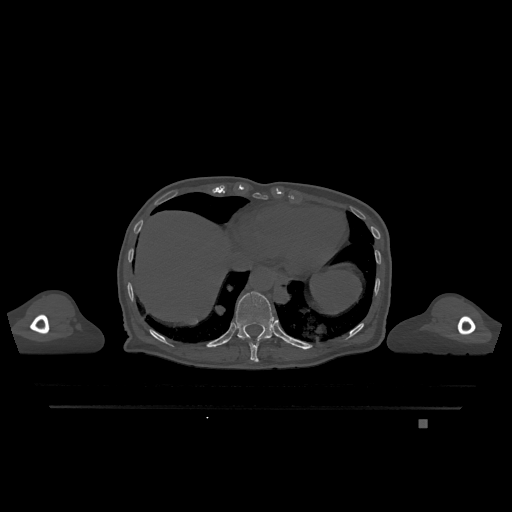
CT including the spine, one axial slice. Position 610 of 1317 along the scan axis. Bone window (W 1800 / L 400 HU). 0.5 mm slice thickness. 512 × 512 image matrix. Patient: female, 74 years. From the clinical record (not read from this slice): primary cancer: lung; vertebrae with lytic lesions (as recorded): T1, T4, T5, T6, L4, L5.
Structures marked on this image (semi-automatic segmentation, software-assisted and operator-edited):
- T10 vertebra: box from (x=239, y=337) to (x=267, y=362) px
- T11 vertebra: (x=228, y=291)–(x=276, y=342)